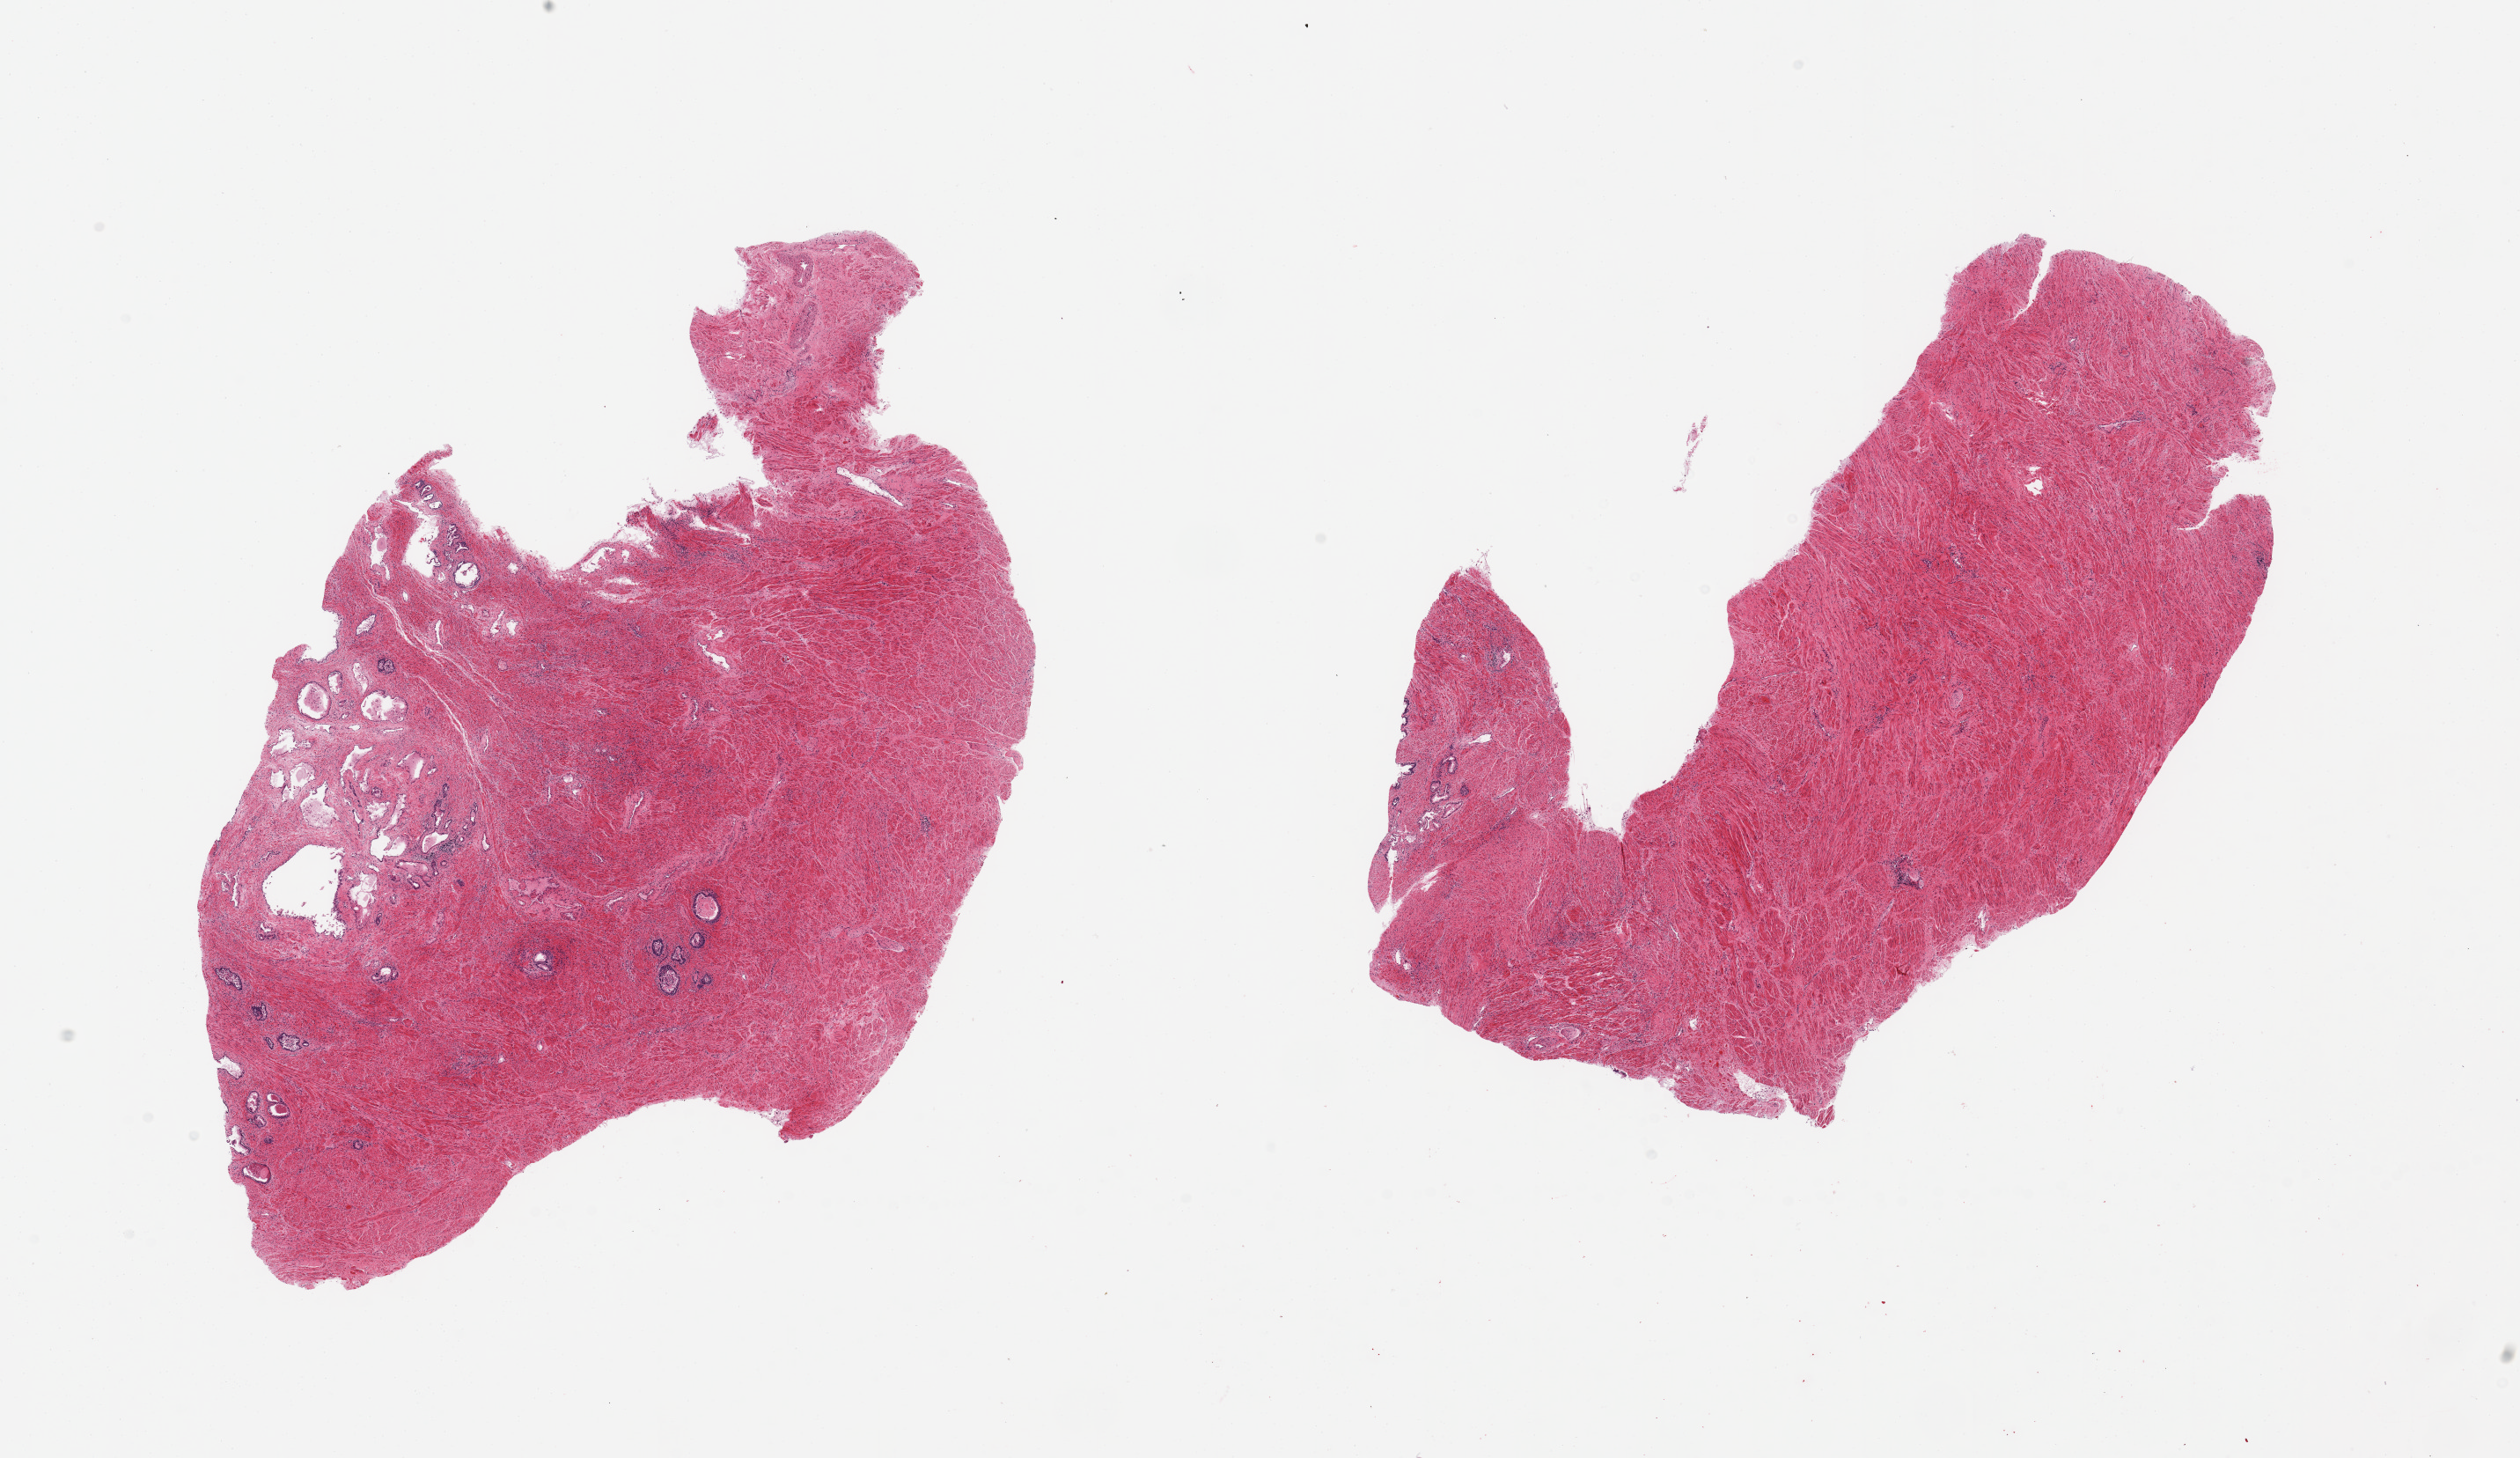
Digitized hematoxylin and eosin (H&E)-stained section, a low-resolution overview of the entire scanned area, about 22.6 x 13.1 mm, PAXgene-fixed, paraffin-embedded tissue, section of prostate (target tissue), donor tissue sample.
Review note (as recorded): 2 pieces; predominantly fibromuscular stroma with few glands and focal mild chronic inflammation.